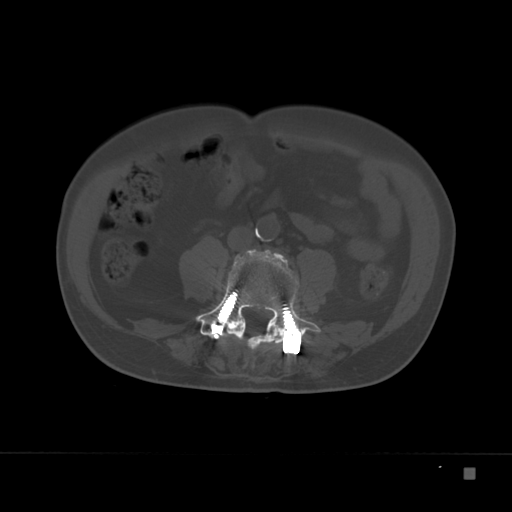
CT including the spine, one axial slice. Position 49 of 332 along the scan axis. Reconstruction kernel Br40s. 120 kVp. Bone window (W 1800 / L 400 HU). 1.5 mm slice thickness. 512 × 512 image matrix. Patient: male, 72 years. From the clinical record (not read from this slice): primary cancer: skeletal.
Outlined on this slice (semi-automatic segmentation, software-assisted and operator-edited):
- L4 vertebra: bounding box (x1, y1, x2, y2) in pixels: (196, 249, 322, 350)